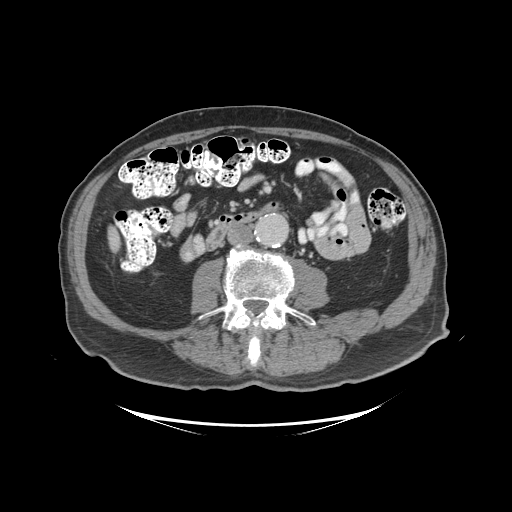
Contrast-enhanced abdominal CT (liver protocol), one axial slice; position 21 of 99 along the scan axis; reconstruction kernel STANDARD; 140 kVp; soft-tissue window (W 400 / L 40 HU); 2.5 mm slice thickness; 512 × 512 image matrix, field of view 460 × 460 mm. From the clinical record (not read from this slice): diagnosis: hepatocellular carcinoma (patient treated with transarterial chemoembolisation; whether this scan precedes or follows treatment is not stated here); TNM stage (as recorded): Stage-I; Child-Pugh class: A.
Outlined on this slice (semi-automatically segmented with operator editing):
- liver parenchyma outside the tumour (the mass and vessels are separate outlines, so this box may not span the whole liver): bounding box <108,228,120,251> (left, top, right, bottom; pixels)